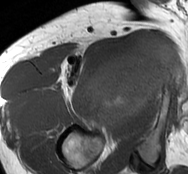
MRI of an extremity soft-tissue mass, one axial slice. Position 63 of 93 along the scan axis. MR volume resampled by the dataset authors to the PET/CT grid (not the native acquisition matrix). 3.27 mm slice thickness. 188 × 174 image matrix, field of view 184 × 170 mm. Male patient. Case-level facts recorded for this patient, not image findings: histological type: undifferentiated - pleiomorphic; grade: high; site of the primary tumour: right thigh.
Outlined on this slice (expert contour drawn on MRI and transferred to this co-registered scan by the dataset authors):
- gross tumour volume including surrounding oedema: bounding box [x1, y1, x2, y2] px = [86, 33, 181, 127]
- gross tumour volume (mass): [86, 35, 180, 129]